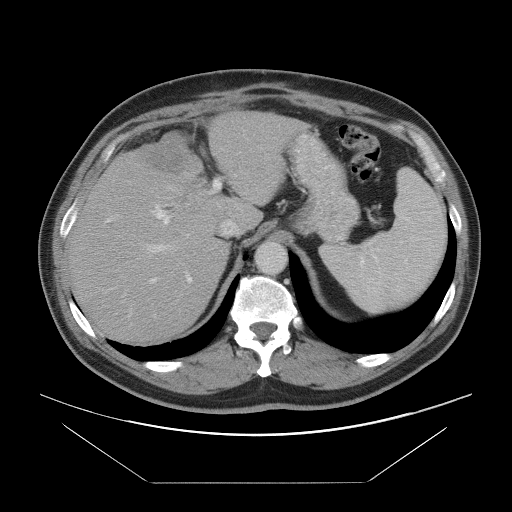
Contrast-enhanced abdominal CT, one axial slice; position 65 of 97 along the scan axis; intravenous contrast given; soft-tissue window (W 400 / L 40 HU); 5 mm slice thickness; 512 × 512 image matrix, field of view 442 × 442 mm. Male patient, age 62 years. From the clinical record (not read from this slice): diagnosis: colorectal cancer liver metastases, imaged before liver resection; multiple liver metastases: no; largest metastasis: 7 cm.
Annotated regions visible in this slice (manually delineated by an expert):
- hepatic veins: bounding box [x1, y1, x2, y2] px = [138, 139, 283, 259]
- liver: [71, 113, 297, 341]
- planned liver remnant (the part of the liver to remain after resection): [71, 172, 233, 340]
- portal vein (with intrahepatic branches): [105, 175, 237, 313]
- liver metastasis: [142, 132, 190, 174]